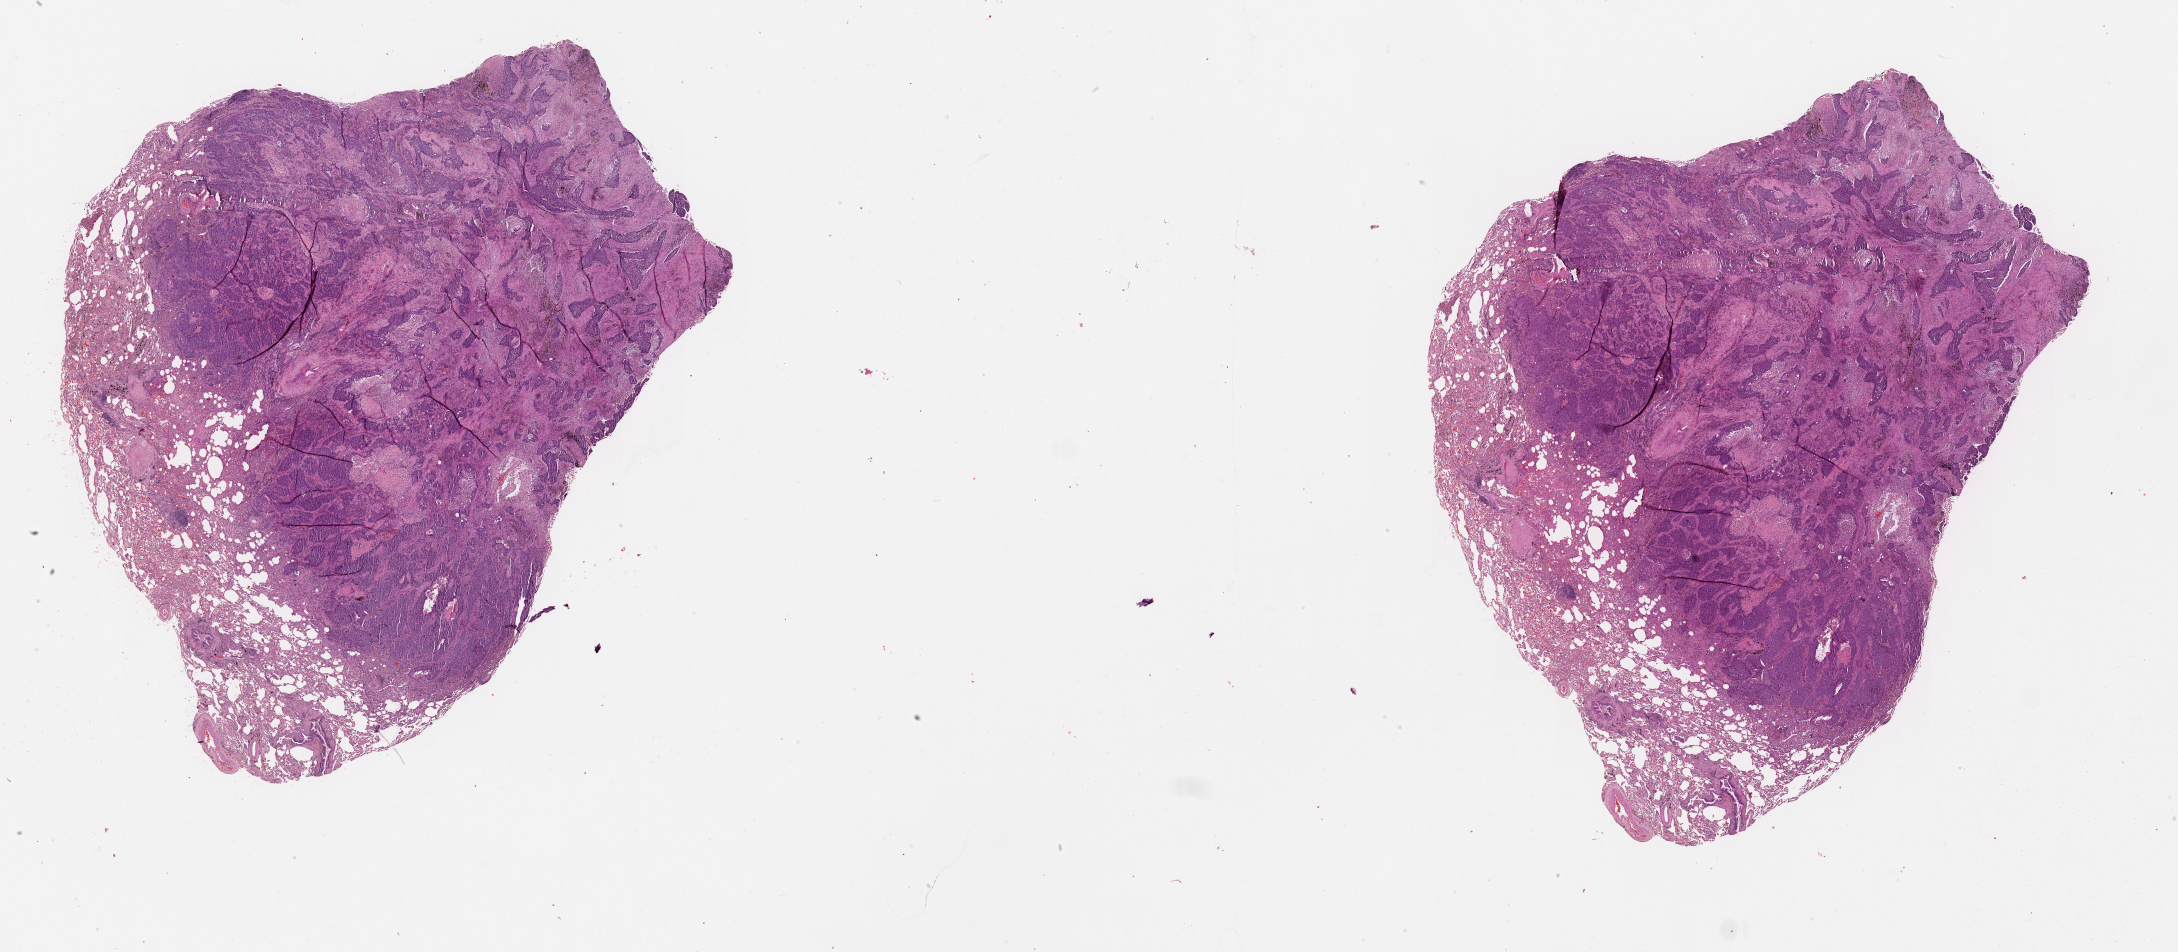
Whole-slide histology image, Hematoxylin and eosin (H&E) stained — shown as a low-resolution overview of the whole scanned area (about 35.1 x 15.3 mm). Tumour tissue sample, lung. 59-year-old male patient.
Patient diagnosis (cohort enrolment): squamous cell carcinoma (lung).